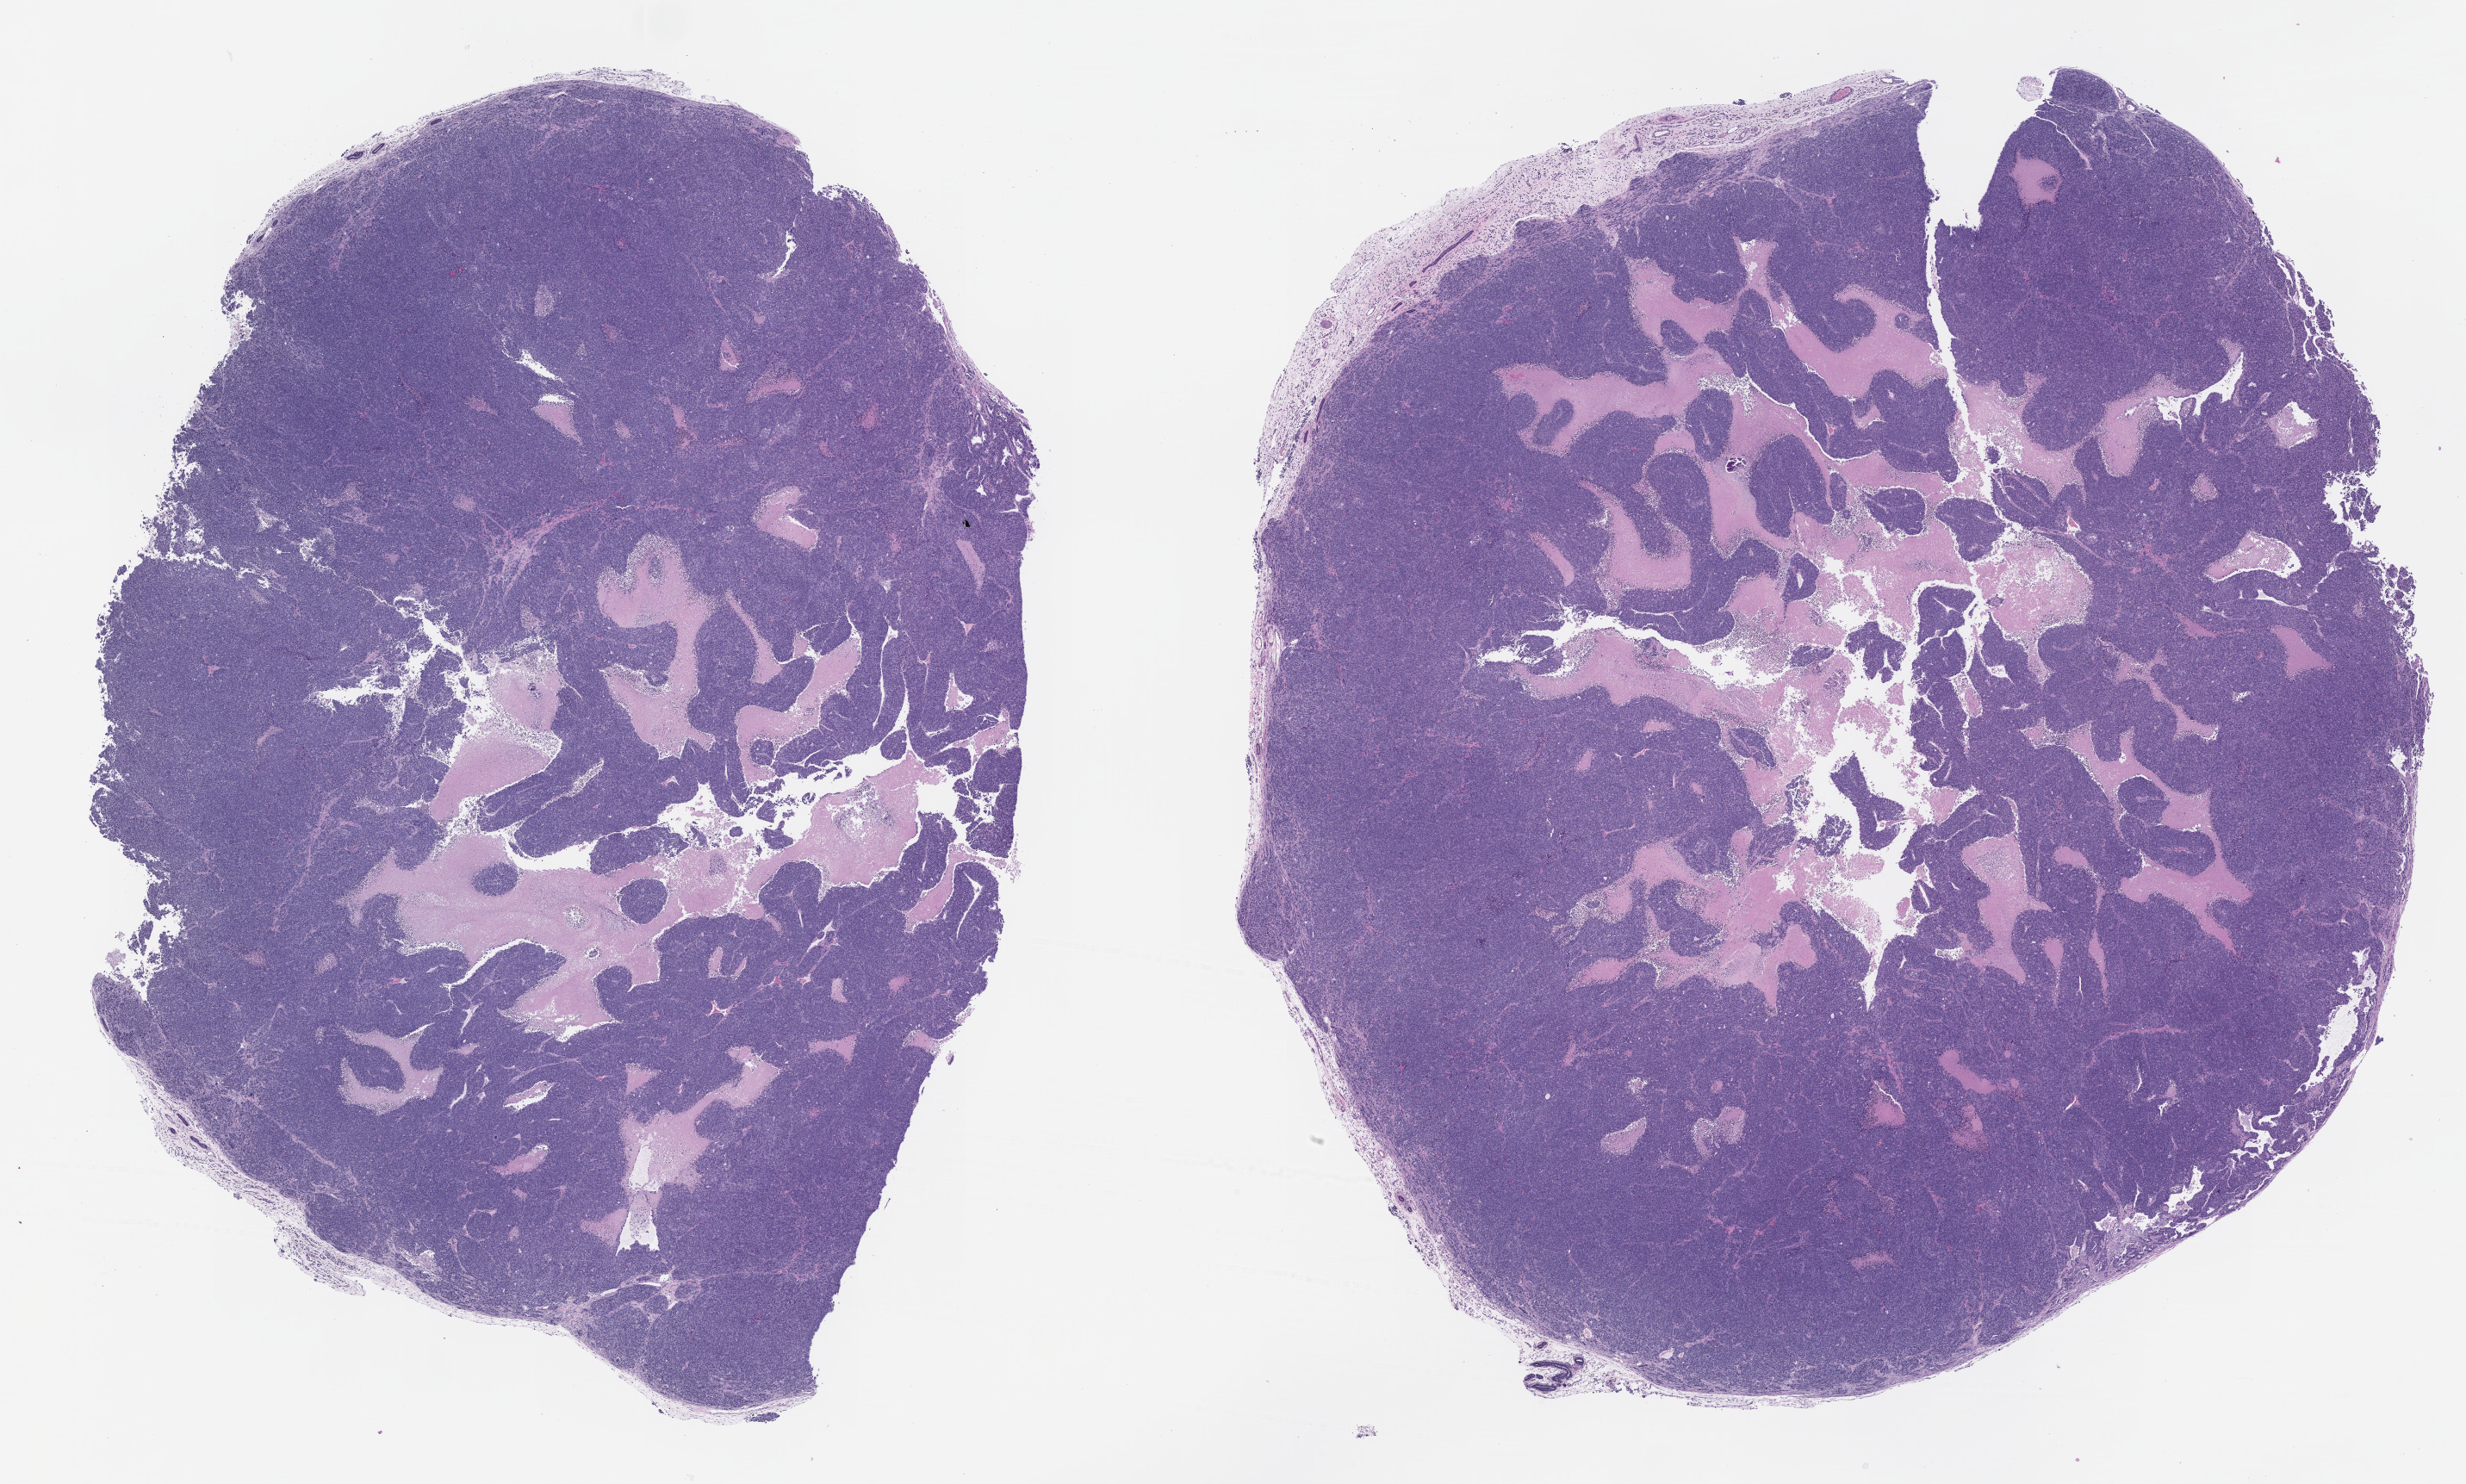
Hematoxylin and eosin (H&E) whole-slide image of a patient-derived xenograft (PDX) tumor grown in a mouse, passage 2 — low-resolution overview of the scanned area, about 23.0 x 13.9 mm; formalin-fixed, paraffin-embedded (FFPE) tissue; tumor site category: cervix.
Originating patient diagnosis: Cervical Adenocarcinoma.